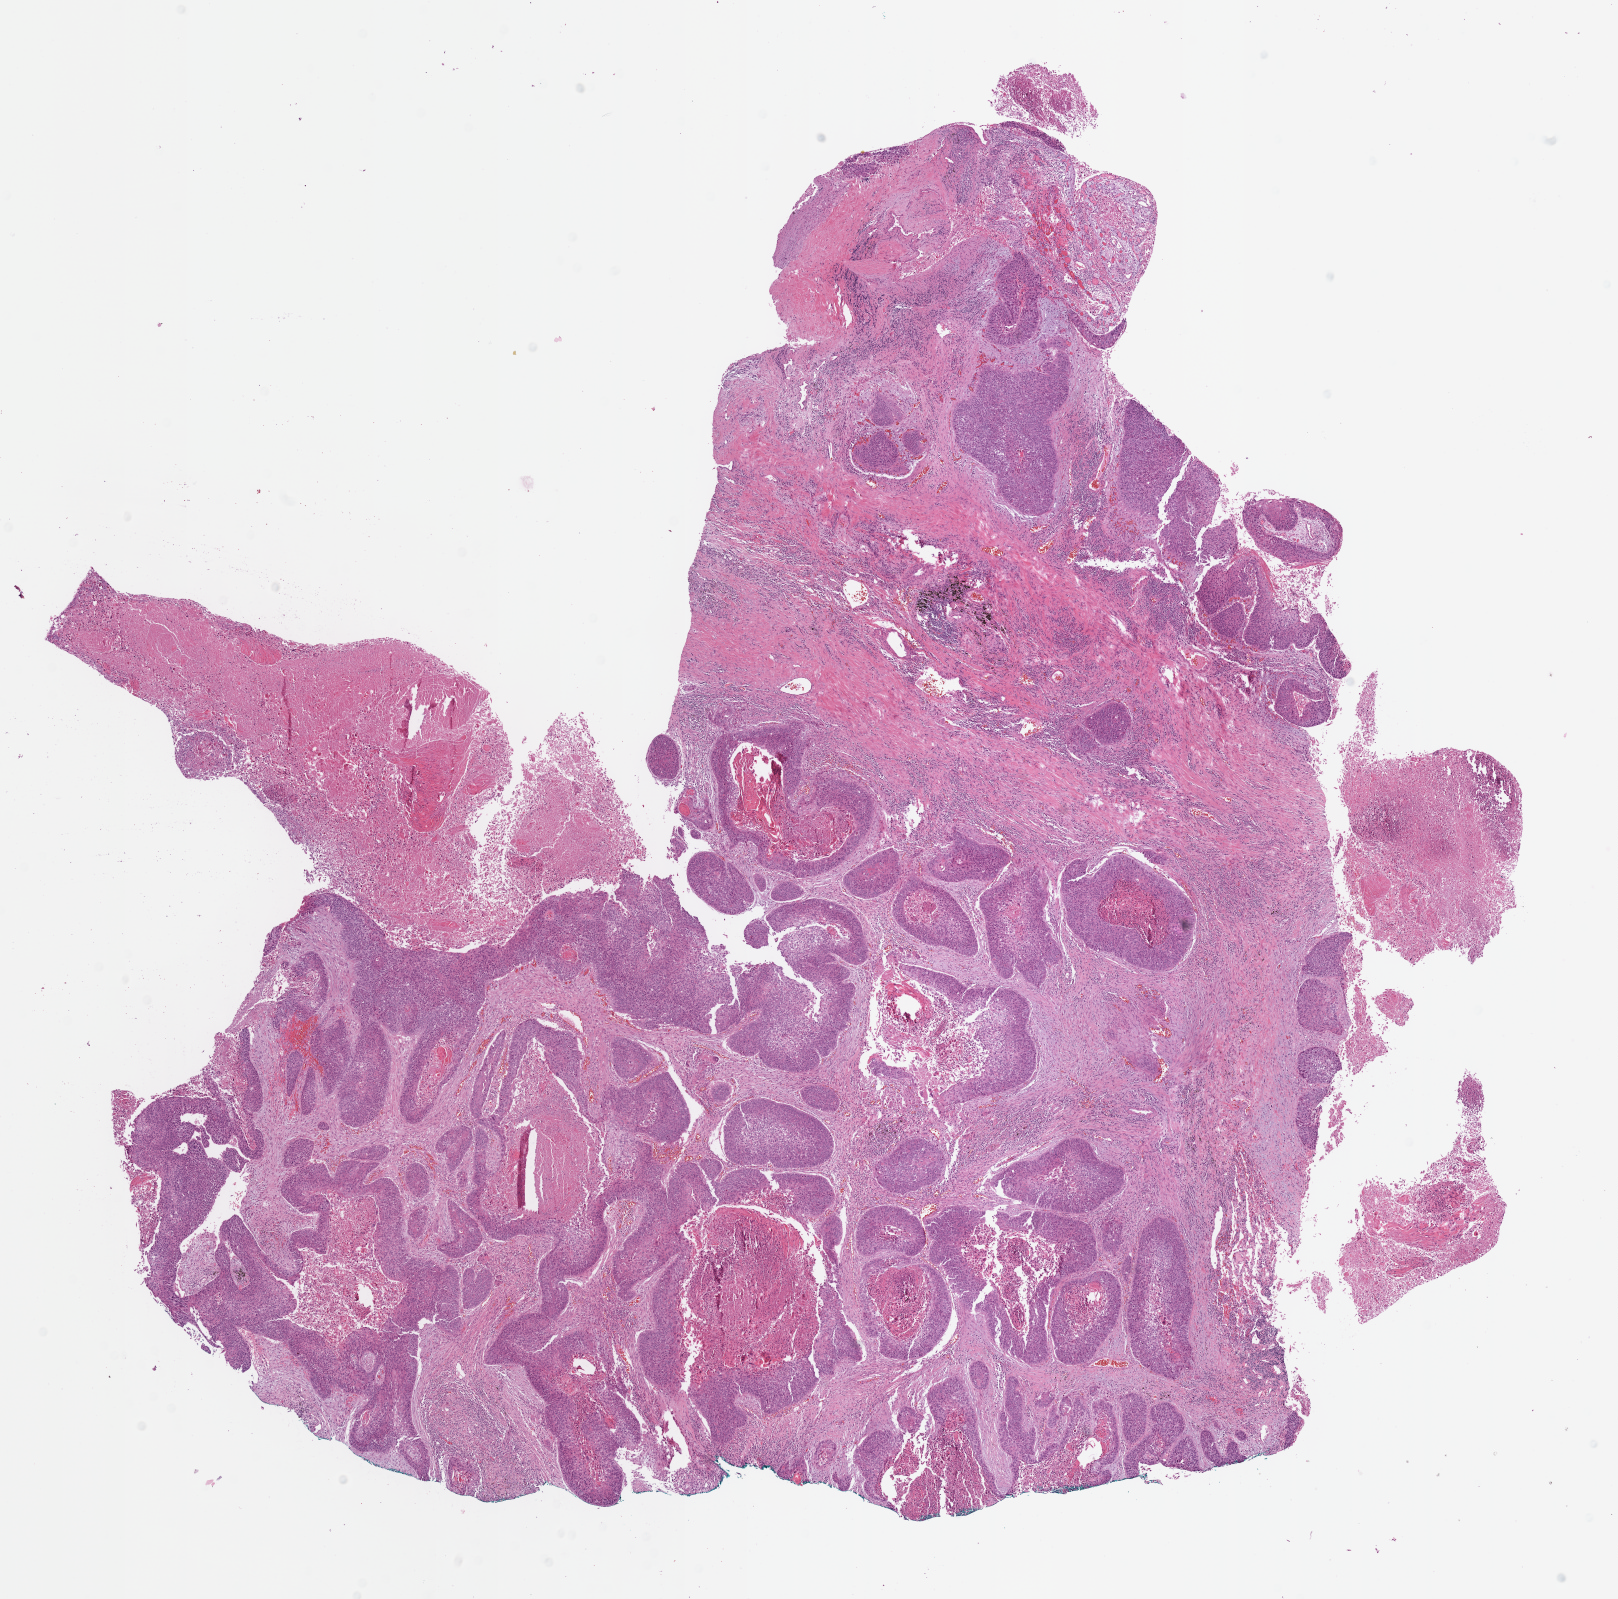
Whole-slide histology image, H&E, whole scanned area (about 12.7 x 12.6 mm, from a 40x scan) shown as a low-resolution overview. Formalin-fixed paraffin-embedded (FFPE) diagnostic section. Lung, primary tumour sample. Male patient; age at initial diagnosis 72 years.
AJCC pathologic stage: IB. Laterality: right. Histologic diagnosis: Squamous cell carcinoma, NOS (upper lobe, lung).